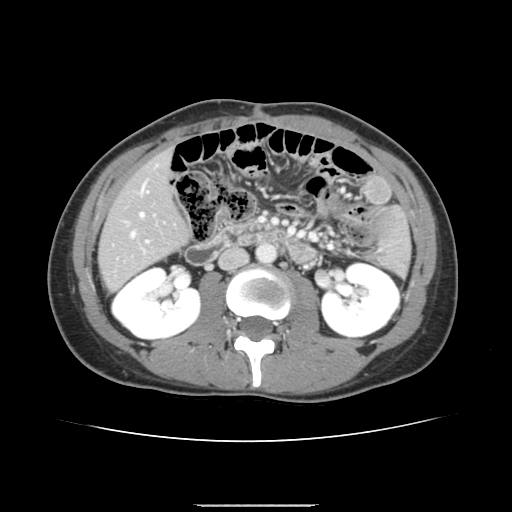
Contrast-enhanced abdominal CT, one axial slice. Position 58 of 150 along the scan axis. Soft-tissue window (W 400 / L 40 HU). 2.5 mm slice thickness. 512 × 512 image matrix. Female patient, age 32 years. From the clinical record (not read from this slice): diagnosis: colorectal cancer liver metastases, imaged before liver resection; multiple liver metastases: yes; largest metastasis: 0.7 cm; disease in both lobes: no.
Annotated regions visible in this slice (expert manual segmentation):
- hepatic veins: bounding box (x1, y1, x2, y2) in pixels: (132, 187, 144, 236)
- liver: (100, 153, 188, 289)
- planned liver remnant (the part of the liver to remain after resection): (100, 153, 188, 289)
- portal vein (with intrahepatic branches): (146, 240, 149, 242)